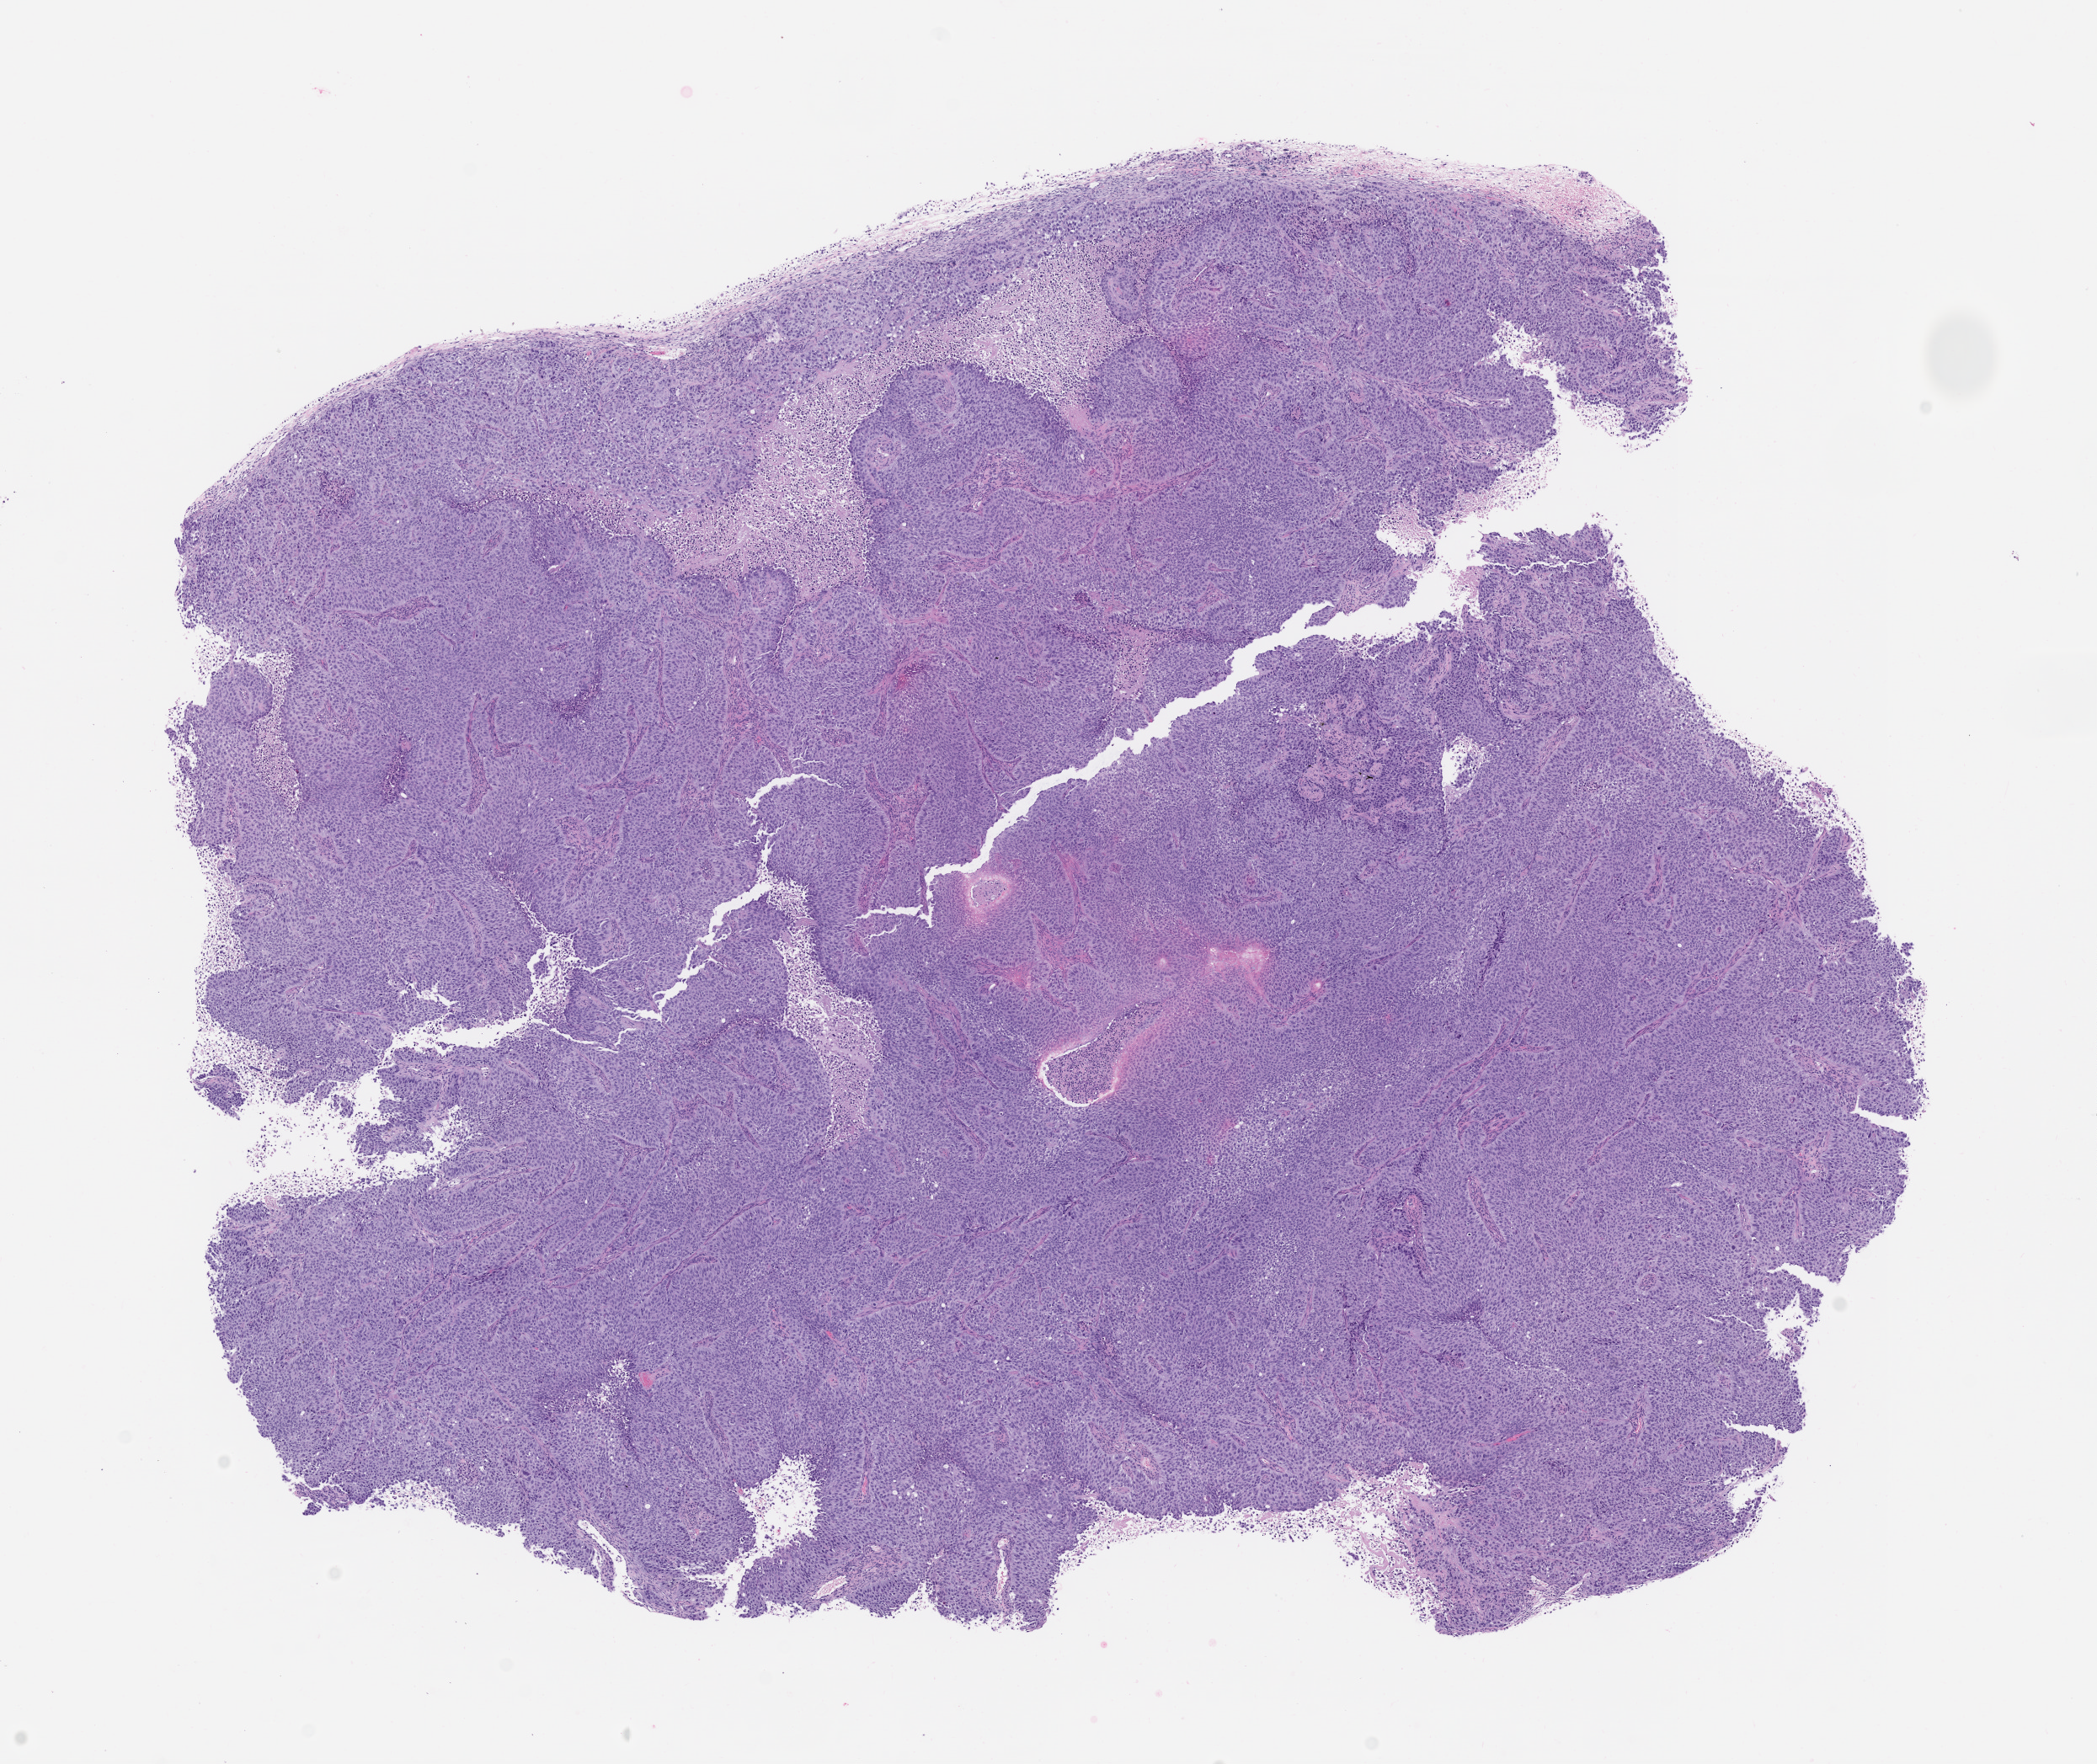
Haematoxylin and eosin whole-slide image of a patient-derived xenograft (PDX) tumor grown in a mouse, passage 1 — whole scanned area (about 10.0 x 8.4 mm) shown as a low-resolution overview. Formalin-fixed, paraffin-embedded (FFPE) tissue. Tumor site category: lung.
Originating patient diagnosis: Lung Squamous Cell Carcinoma.